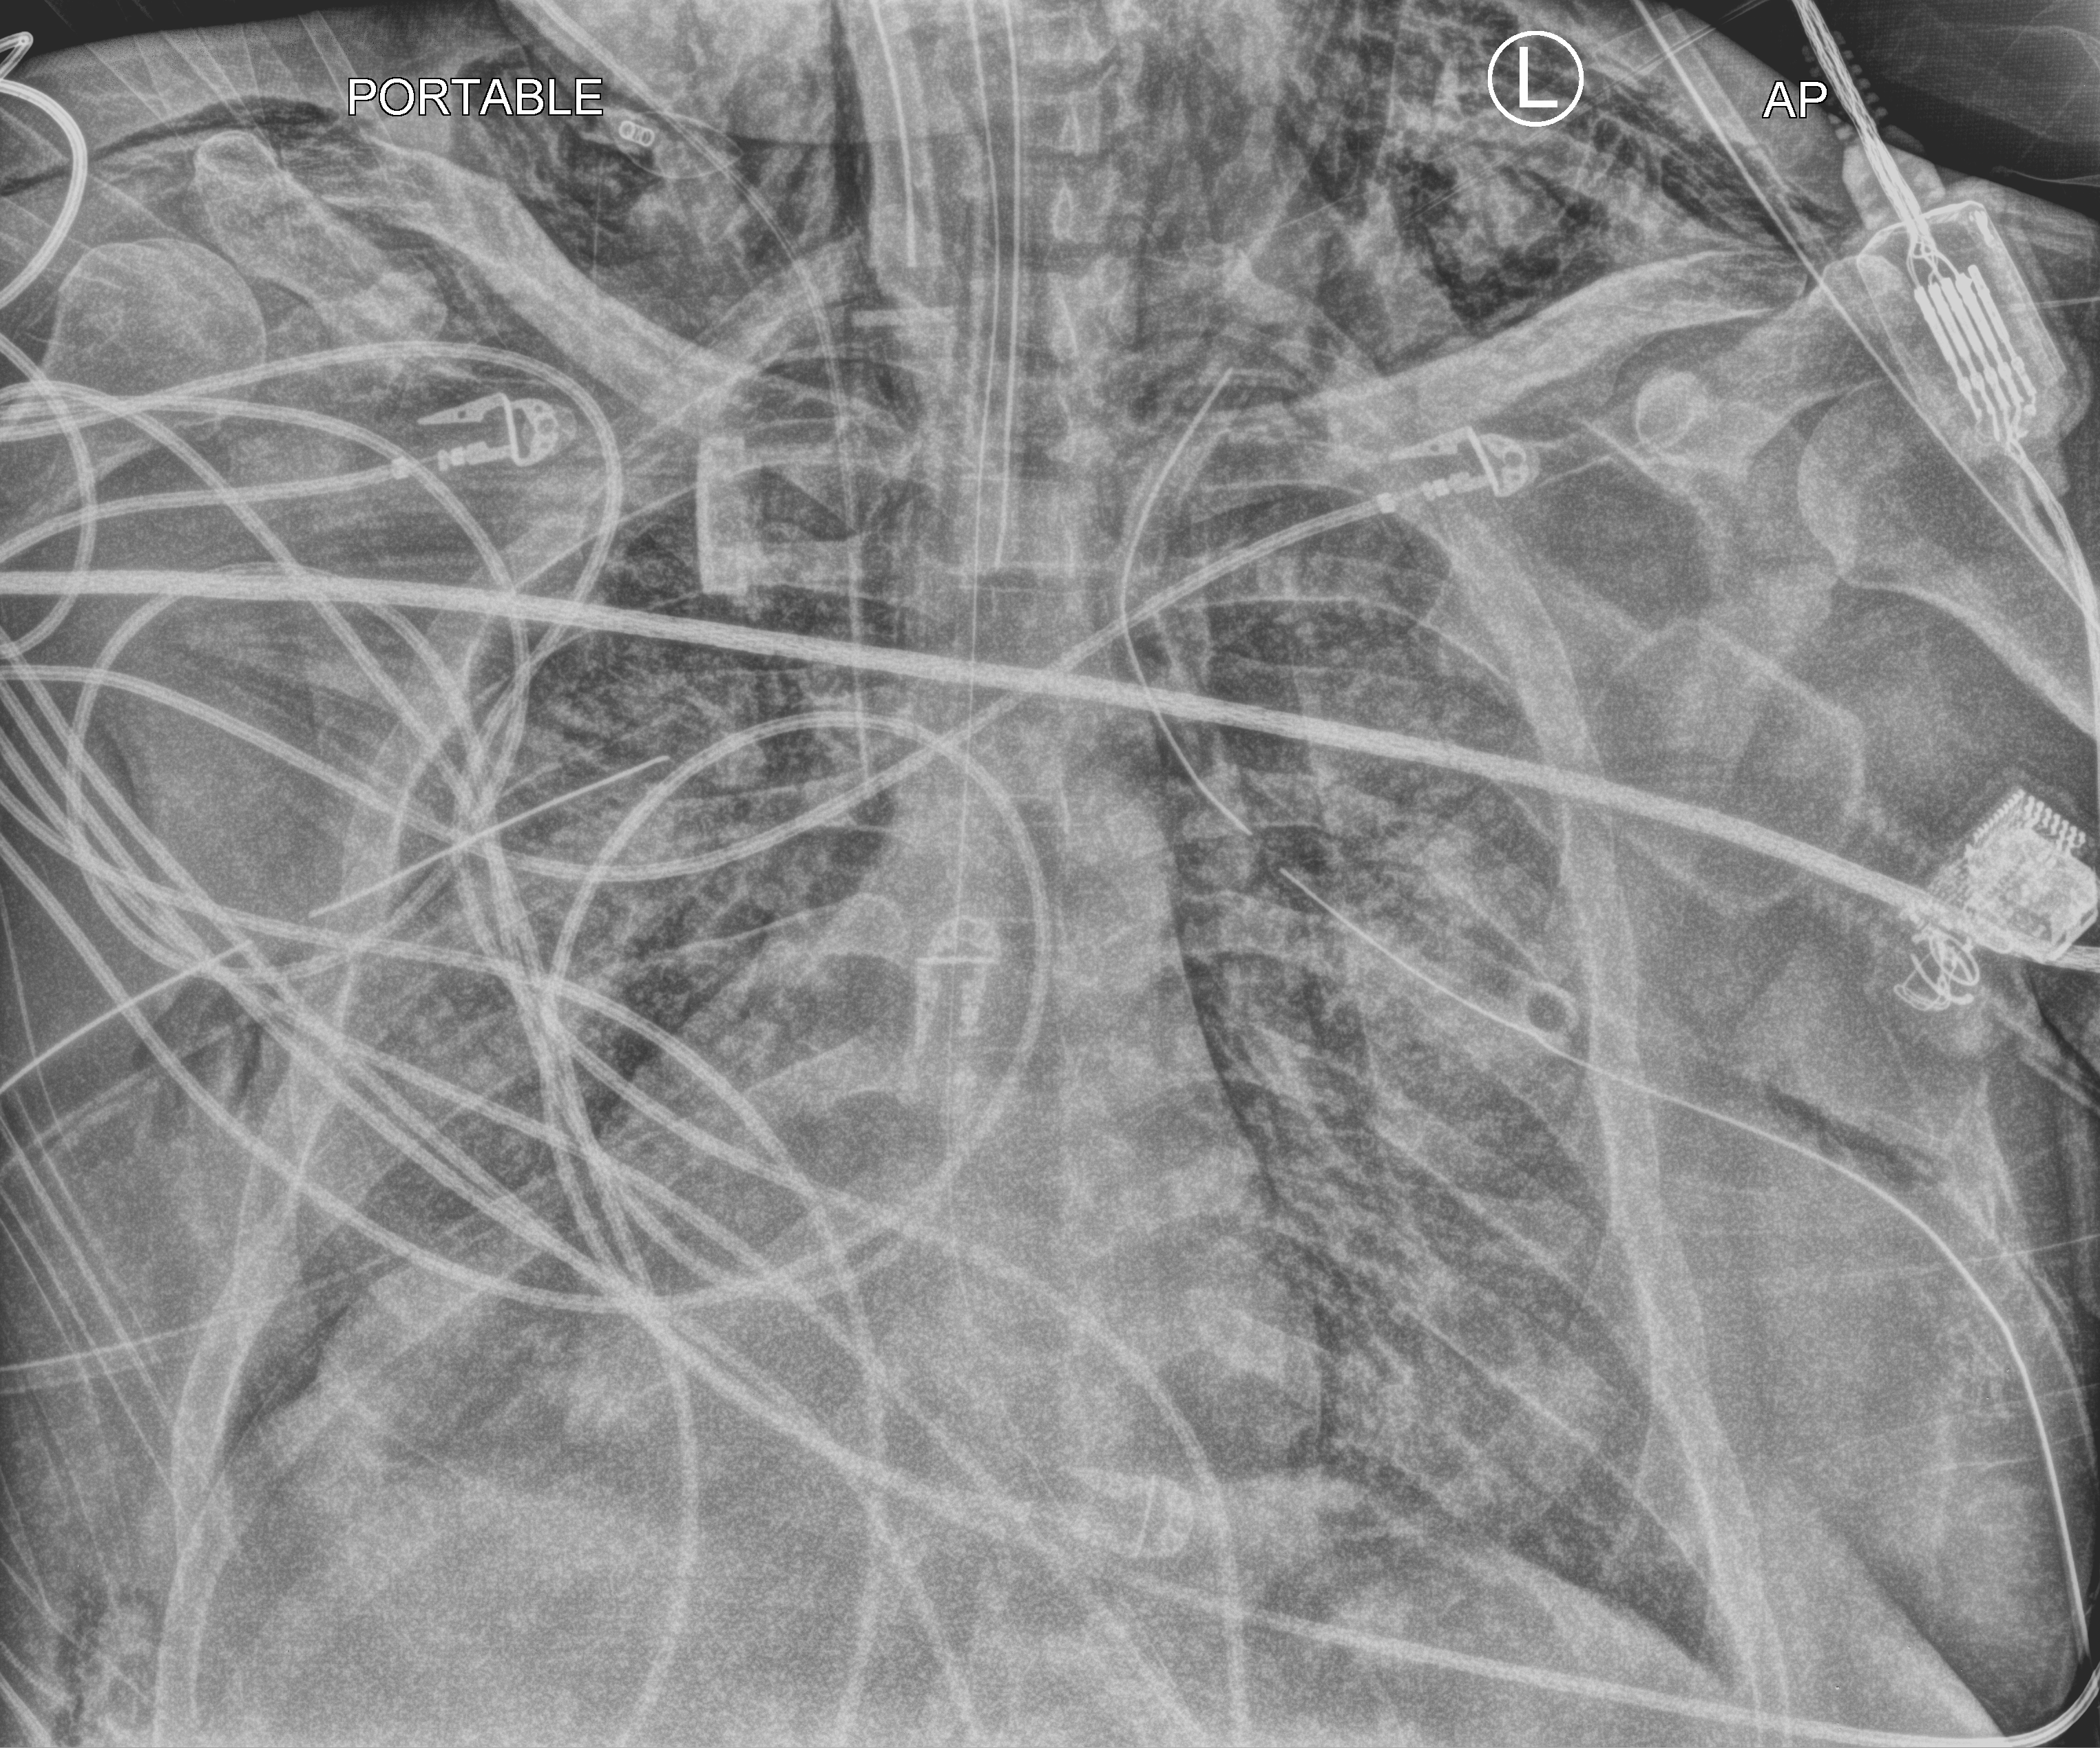
Portable chest radiograph, anteroposterior (AP) projection. Patient hospitalised with COVID-19, aged 18–59 years.
Hospital-stay facts (about this admission, not read from this image; timing relative to this image not recorded):
- admitted to intensive care during this hospital stay: yes